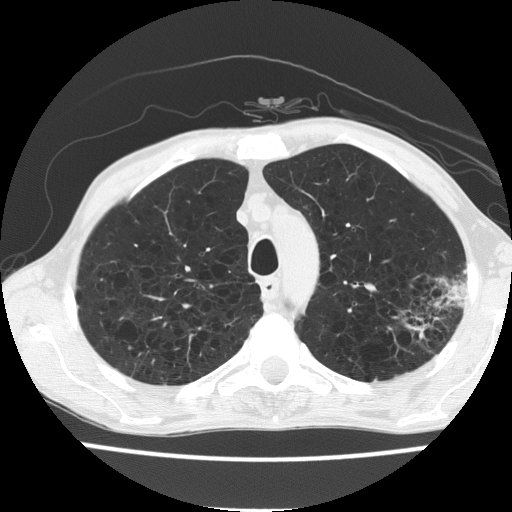
Axial slice from a low-dose chest CT screening exam. Baseline screening round. Lung window (W 1500 / L -600 HU). 2 mm slice thickness. Slice 43 of 187 in the series. 512 × 512 image matrix. Male, age 60 years at enrolment.
Expert reader's lesion annotation, bounding box <392,263,470,343> (left, top, right, bottom; pixels). Screening reader's record for this exam: no non-calcified nodule ≥4 mm recorded. Official screen result: negative screen, minor abnormalities not suspicious for lung cancer. Lung cancer was diagnosed 490 days after this screen: bronchiolo-alveolar carcinoma, mucinous, left upper lobe, stage IV (AJCC 6th edition).